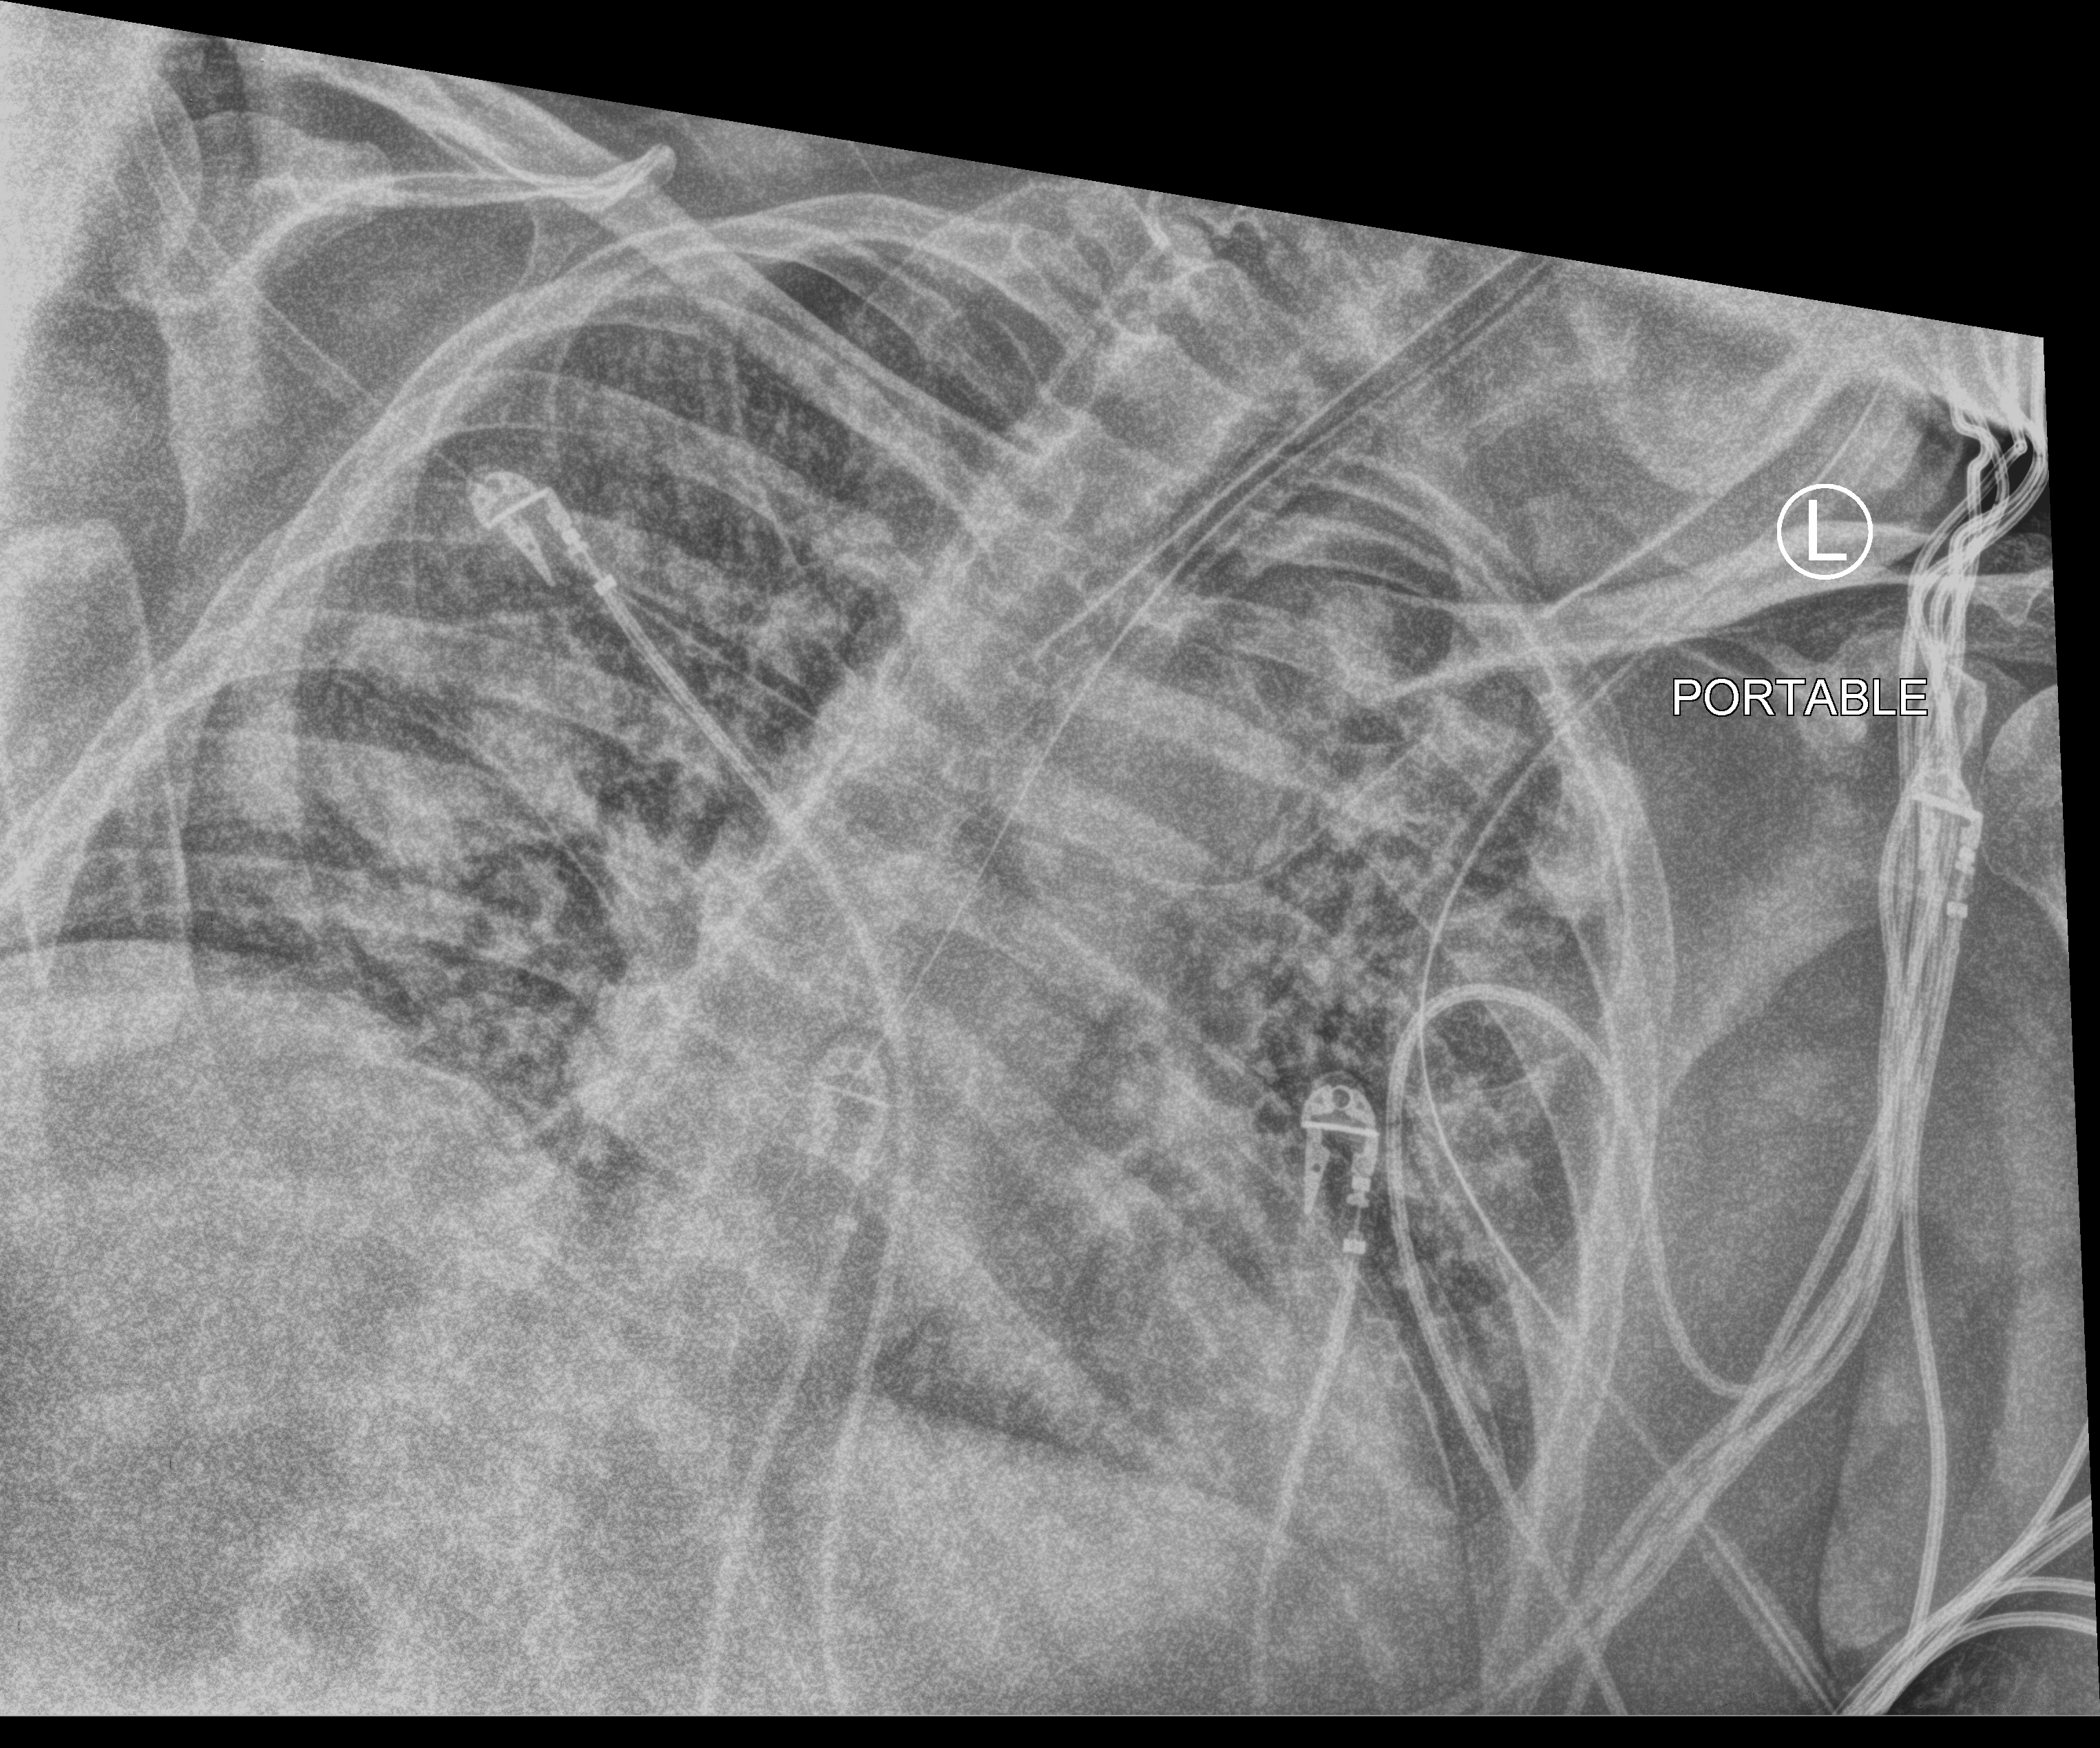
Portable chest radiograph; anteroposterior (AP) projection. Male patient hospitalised with COVID-19, age 60–74 years.
Hospital-stay facts (about this admission, not read from this image; timing relative to this image not recorded):
- admitted to intensive care during this hospital stay: yes
- hypertension (admission record): yes
- chronic kidney disease (admission record): no